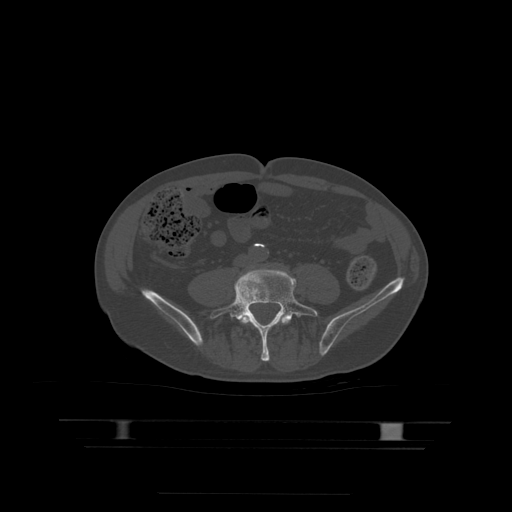
CT including the spine, one axial slice. Position 78 of 522 along the scan axis. Bone window (W 1800 / L 400 HU). 1.25 mm slice thickness. 512 × 512 image matrix, field of view 436 × 436 mm. Patient age 68 years. Case-level facts recorded for this patient, not image findings: primary cancer: urothelial.
Outlined on this slice (semi-automatically segmented with operator editing):
- L4 vertebra: bounding box [x1, y1, x2, y2] px = [241, 317, 290, 325]
- L5 vertebra: [210, 270, 319, 362]